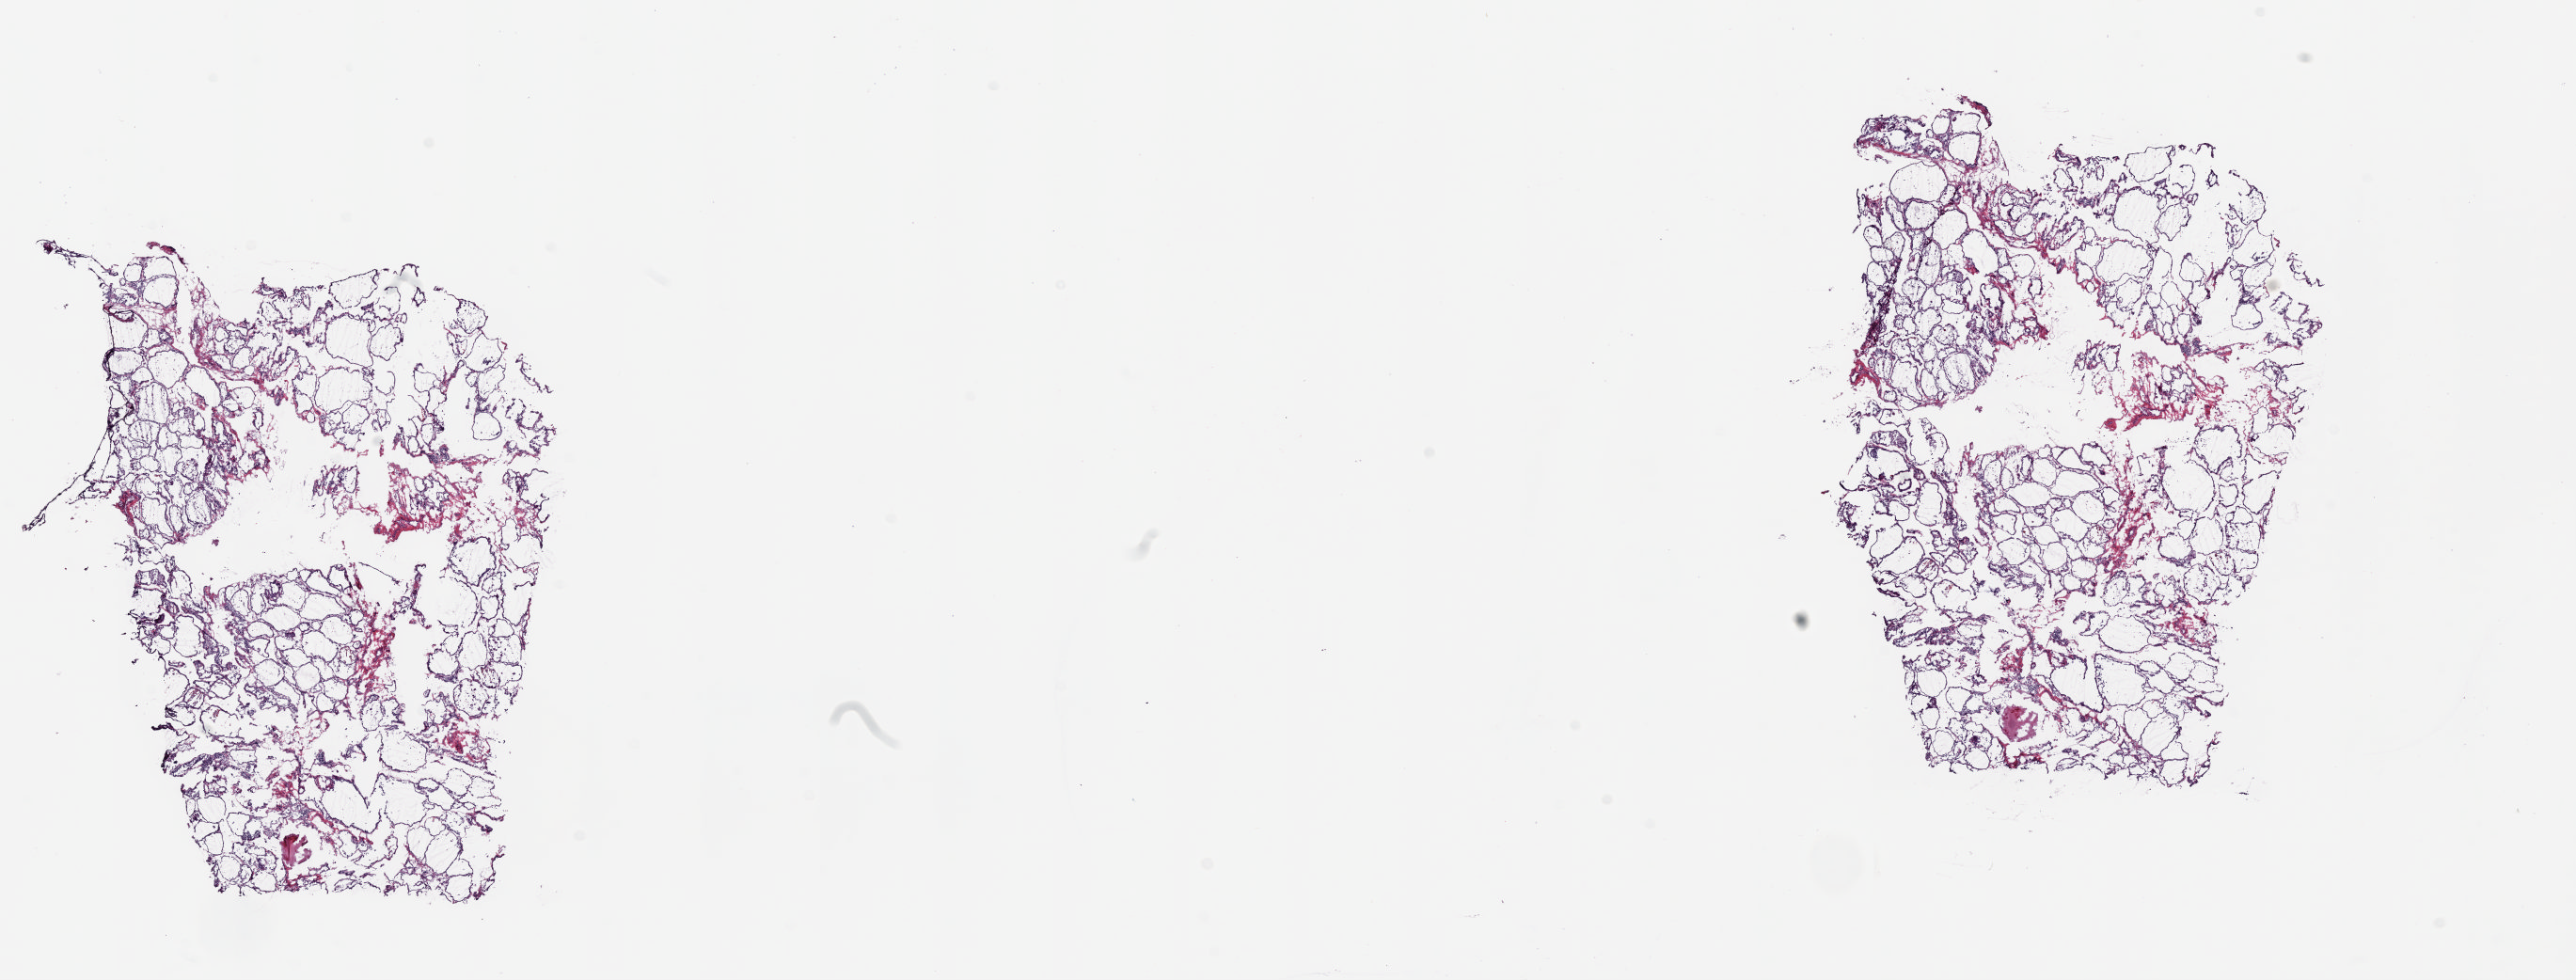
Whole-slide histology image, H&E, a low-resolution overview of the entire scanned area, about 21.6 x 8.2 mm. Frozen section from the top of the tissue portion. Thyroid, solid tissue normal (non-tumour tissue) sample. Female patient; age at initial diagnosis 24 years.
This section: solid tissue normal (non-tumour) sample from the same patient. Patient diagnosis: Papillary adenocarcinoma, NOS (thyroid gland).